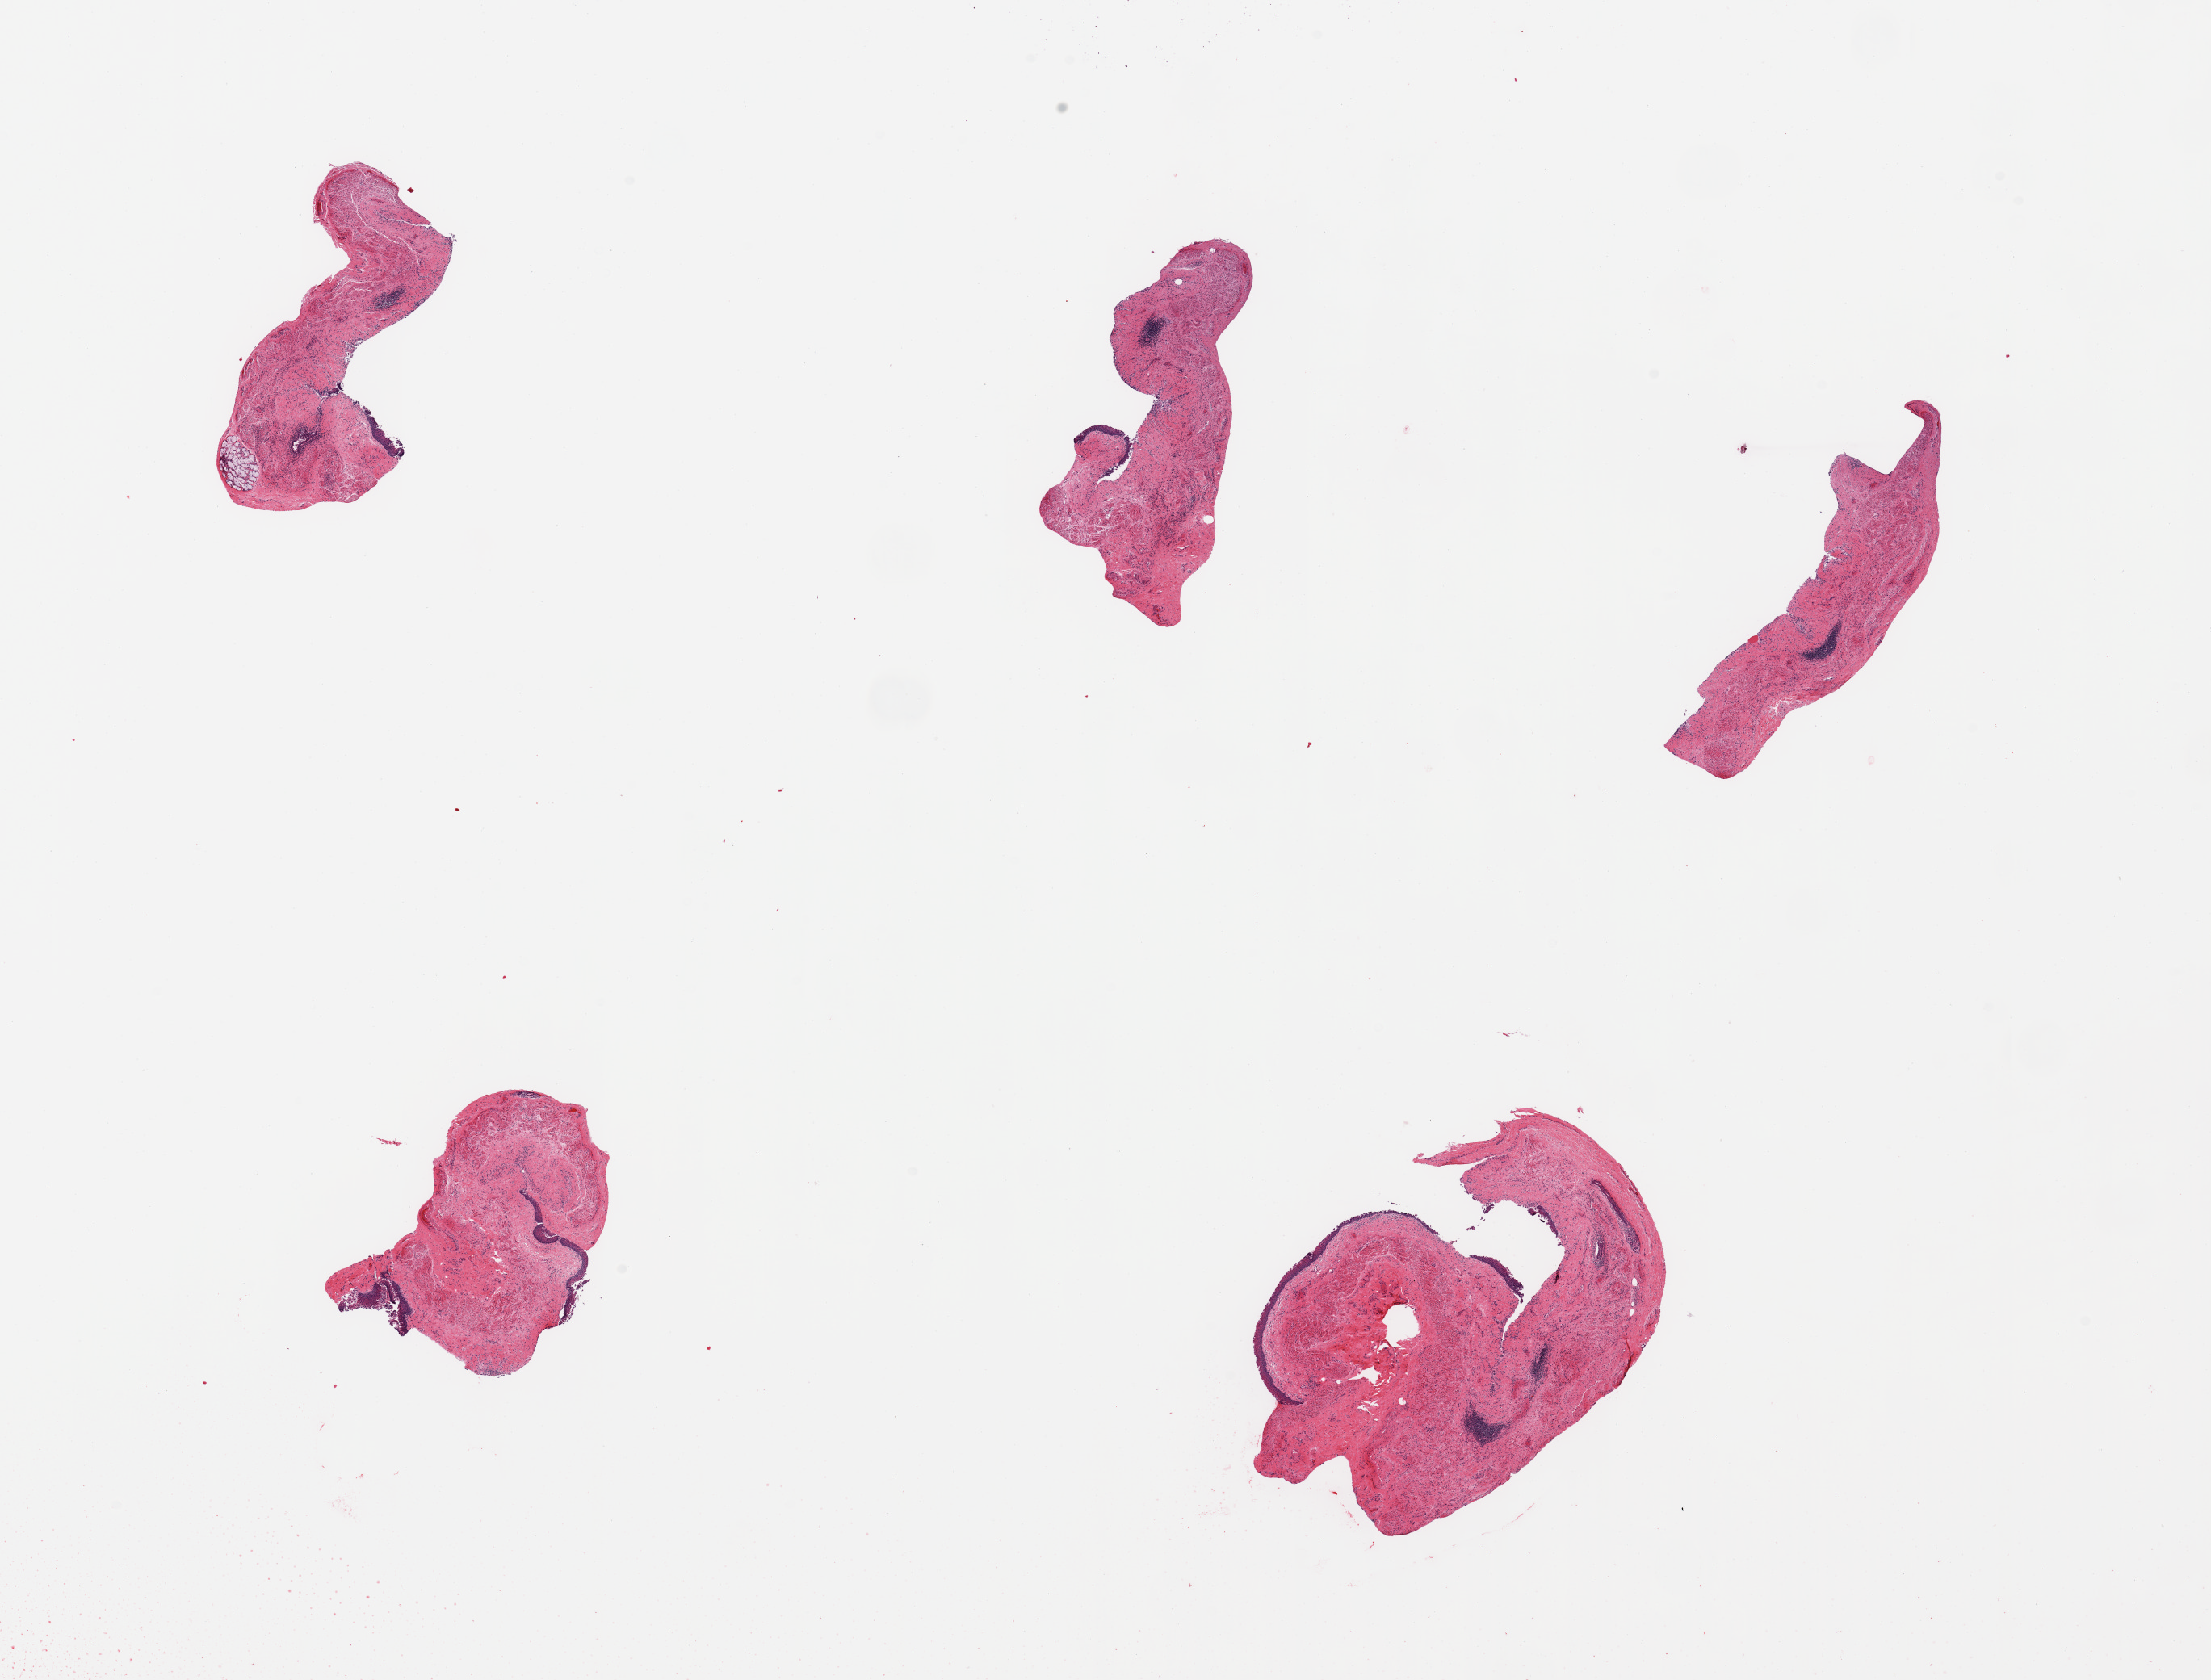
H&E whole-slide image, brightfield — a low-resolution overview of the entire scanned area, about 21.7 x 16.5 mm, PAXgene-fixed, paraffin-embedded tissue, target tissue: esophageal mucous membrane, tissue donor sample. Male donor.
Review note (as recorded): 5 pieces; squamous mucosa is largely sloughed.